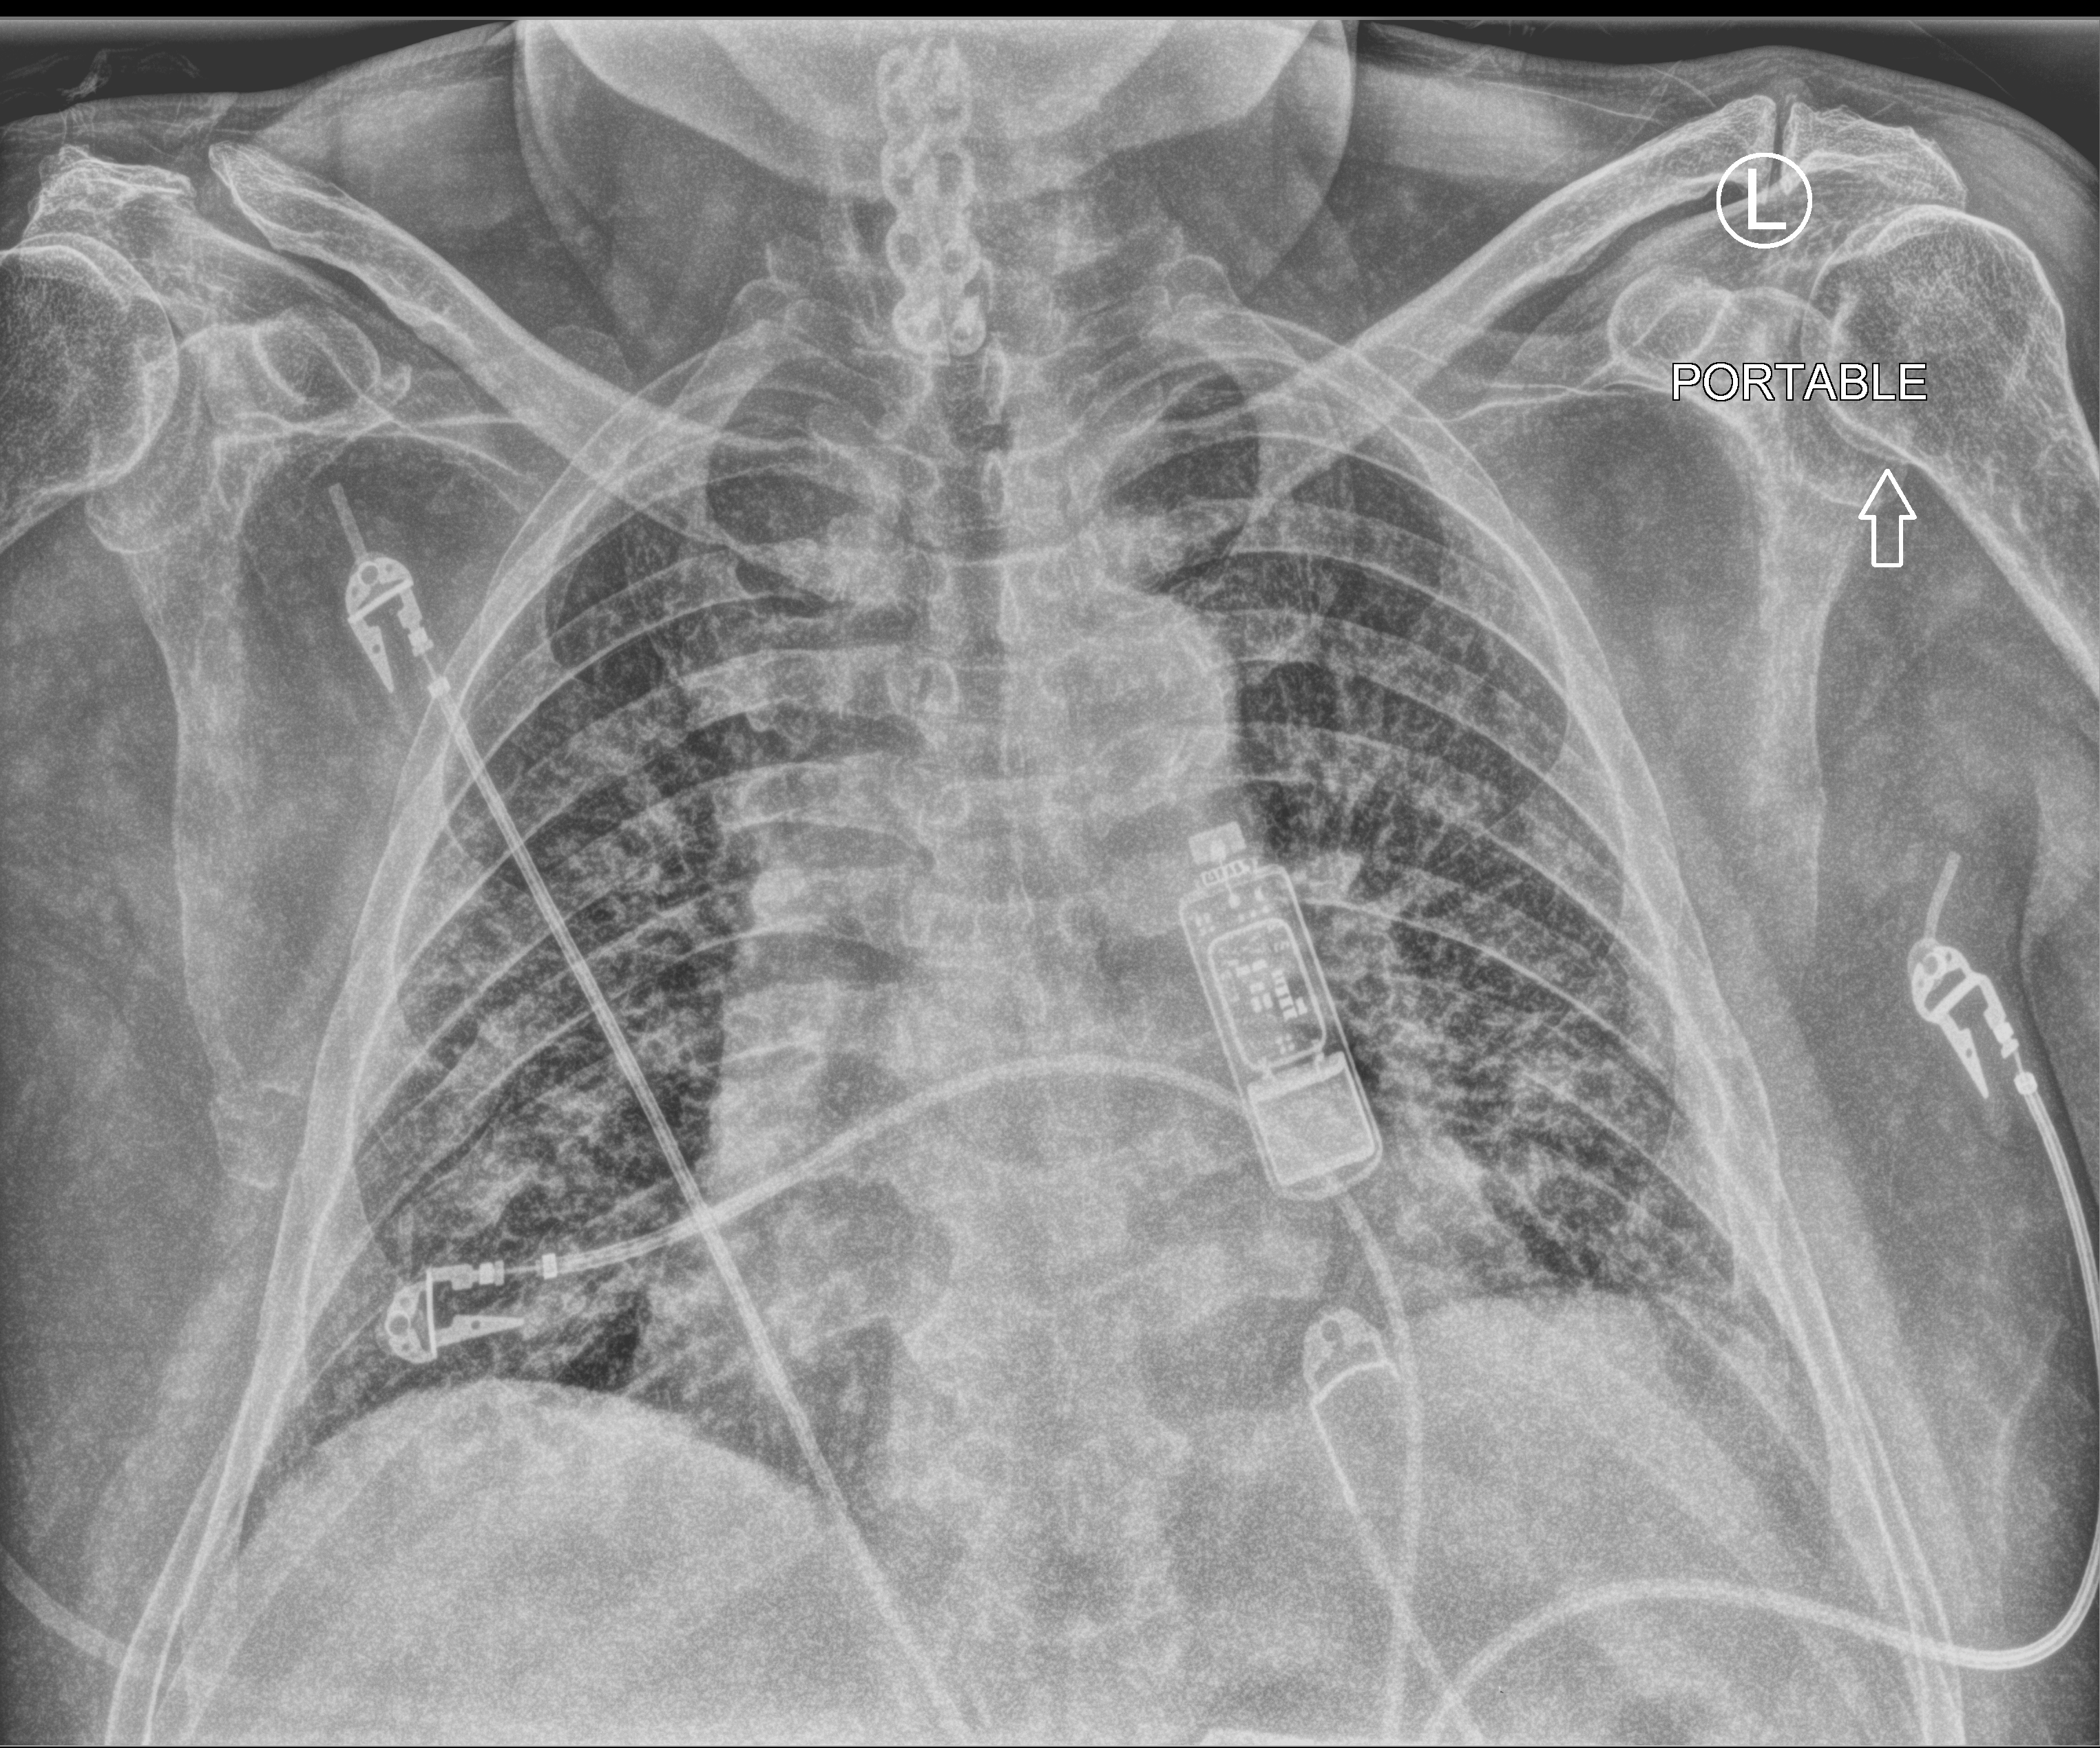
Portable chest radiograph; anteroposterior (AP) projection. Patient hospitalised with COVID-19; male, aged 60–74 years.
Hospital-stay facts (about this admission, not read from this image; timing relative to this image not recorded):
- smoking status (admission record): former